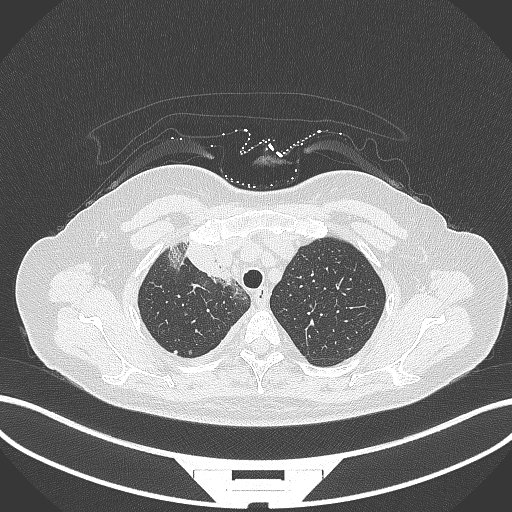
Chest CT, one axial slice; position 253 of 305 along the scan axis; reconstruction kernel B70f; 120 kVp; lung window (W 1500 / L -600 HU); 1 mm slice thickness; 512 × 512 image matrix, field of view 400 × 400 mm. Patient: female, 52 years. Case-level facts recorded for this patient, not image findings: clinical TNM (as recorded): T3 N1 M1.
Annotated regions visible in this slice (rectangle marked by the reading radiologist):
- lung tumour (recorded histology: adenocarcinoma): bounding box [x1, y1, x2, y2] px = [169, 237, 235, 285]